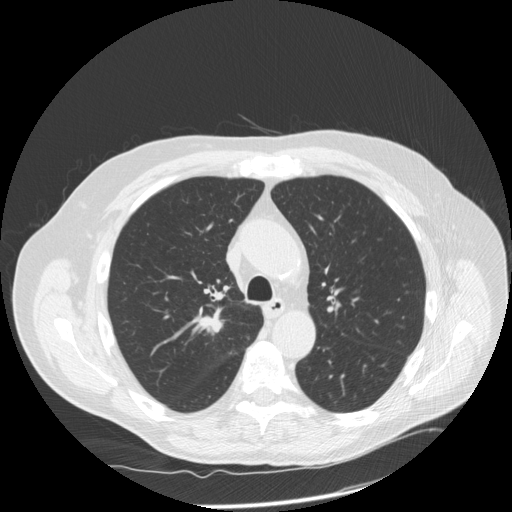
Low-dose screening chest CT, axial slice. Third screening round (two years after baseline). Lung window (W 1500 / L -600 HU). 2.5 mm slice thickness. 120 kVp. Male participant, aged 69 years at enrolment.
Expert reader's lesion annotation, box from (x=184, y=298) to (x=242, y=348) px. Screening reader's record for this exam (one nodule recorded; not confirmed to be the boxed lesion): non-calcified nodule or mass ≥4 mm, right upper lobe, 18 × 17 mm, spiculated (stellate) margins, soft tissue attenuation, pre-existing on the prior screen: no. Official screen result: positive, other. Later outcome: lung cancer diagnosed 13 days after this screen — squamous cell carcinoma, NOS, right upper lobe, poorly differentiated (G3), stage IA (AJCC 6th edition), 22 mm at pathology.